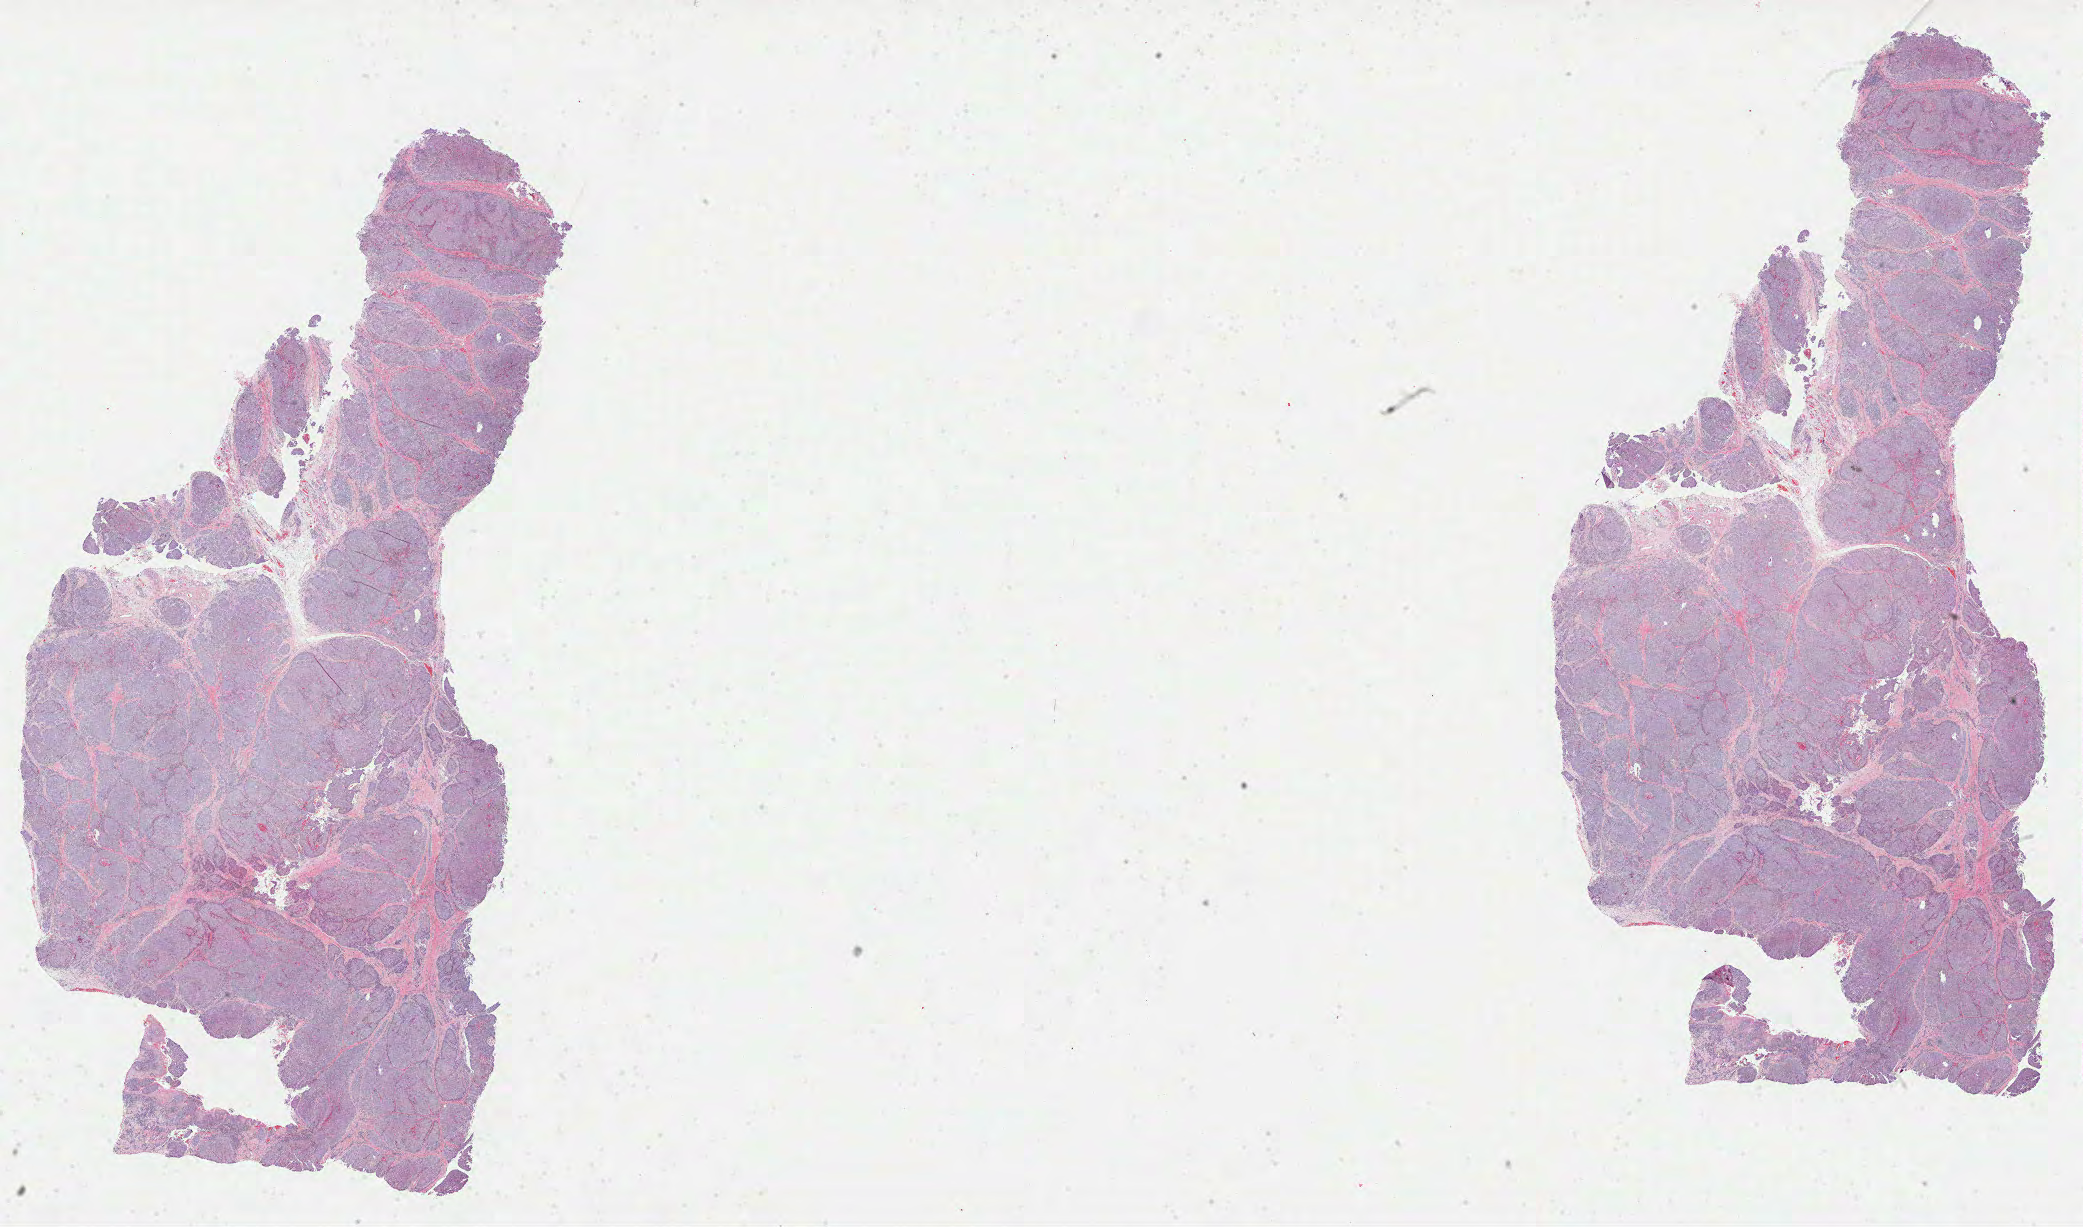
Whole-slide histology image, H&E, shown as a low-resolution overview of the whole scanned area (about 33.6 x 19.8 mm, acquisition: 40x scan), formalin-fixed paraffin-embedded (FFPE) diagnostic section, sample: primary tumour, head and neck. Male, age 73 years at initial diagnosis.
Pathologic diagnosis: Squamous cell carcinoma, NOS (larynx, NOS).